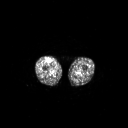
FDG PET of an extremity soft-tissue mass (from a PET/CT study), one axial slice; slice 233 of 311 in the series (ordered by position); 3.27 mm slice thickness; 128 × 128 image matrix, field of view 700 × 700 mm. Male patient, age 56 years. Case-level facts recorded for this patient, not image findings: histological type: pleiomorphic leiomyosarcoma; grade: intermediate; site of the primary tumour: right thigh.
Outlined on this slice (expert contour drawn on MRI and transferred to this co-registered scan by the dataset authors):
- gross tumour volume including surrounding oedema: bounding box [x1, y1, x2, y2] px = [46, 59, 51, 62]